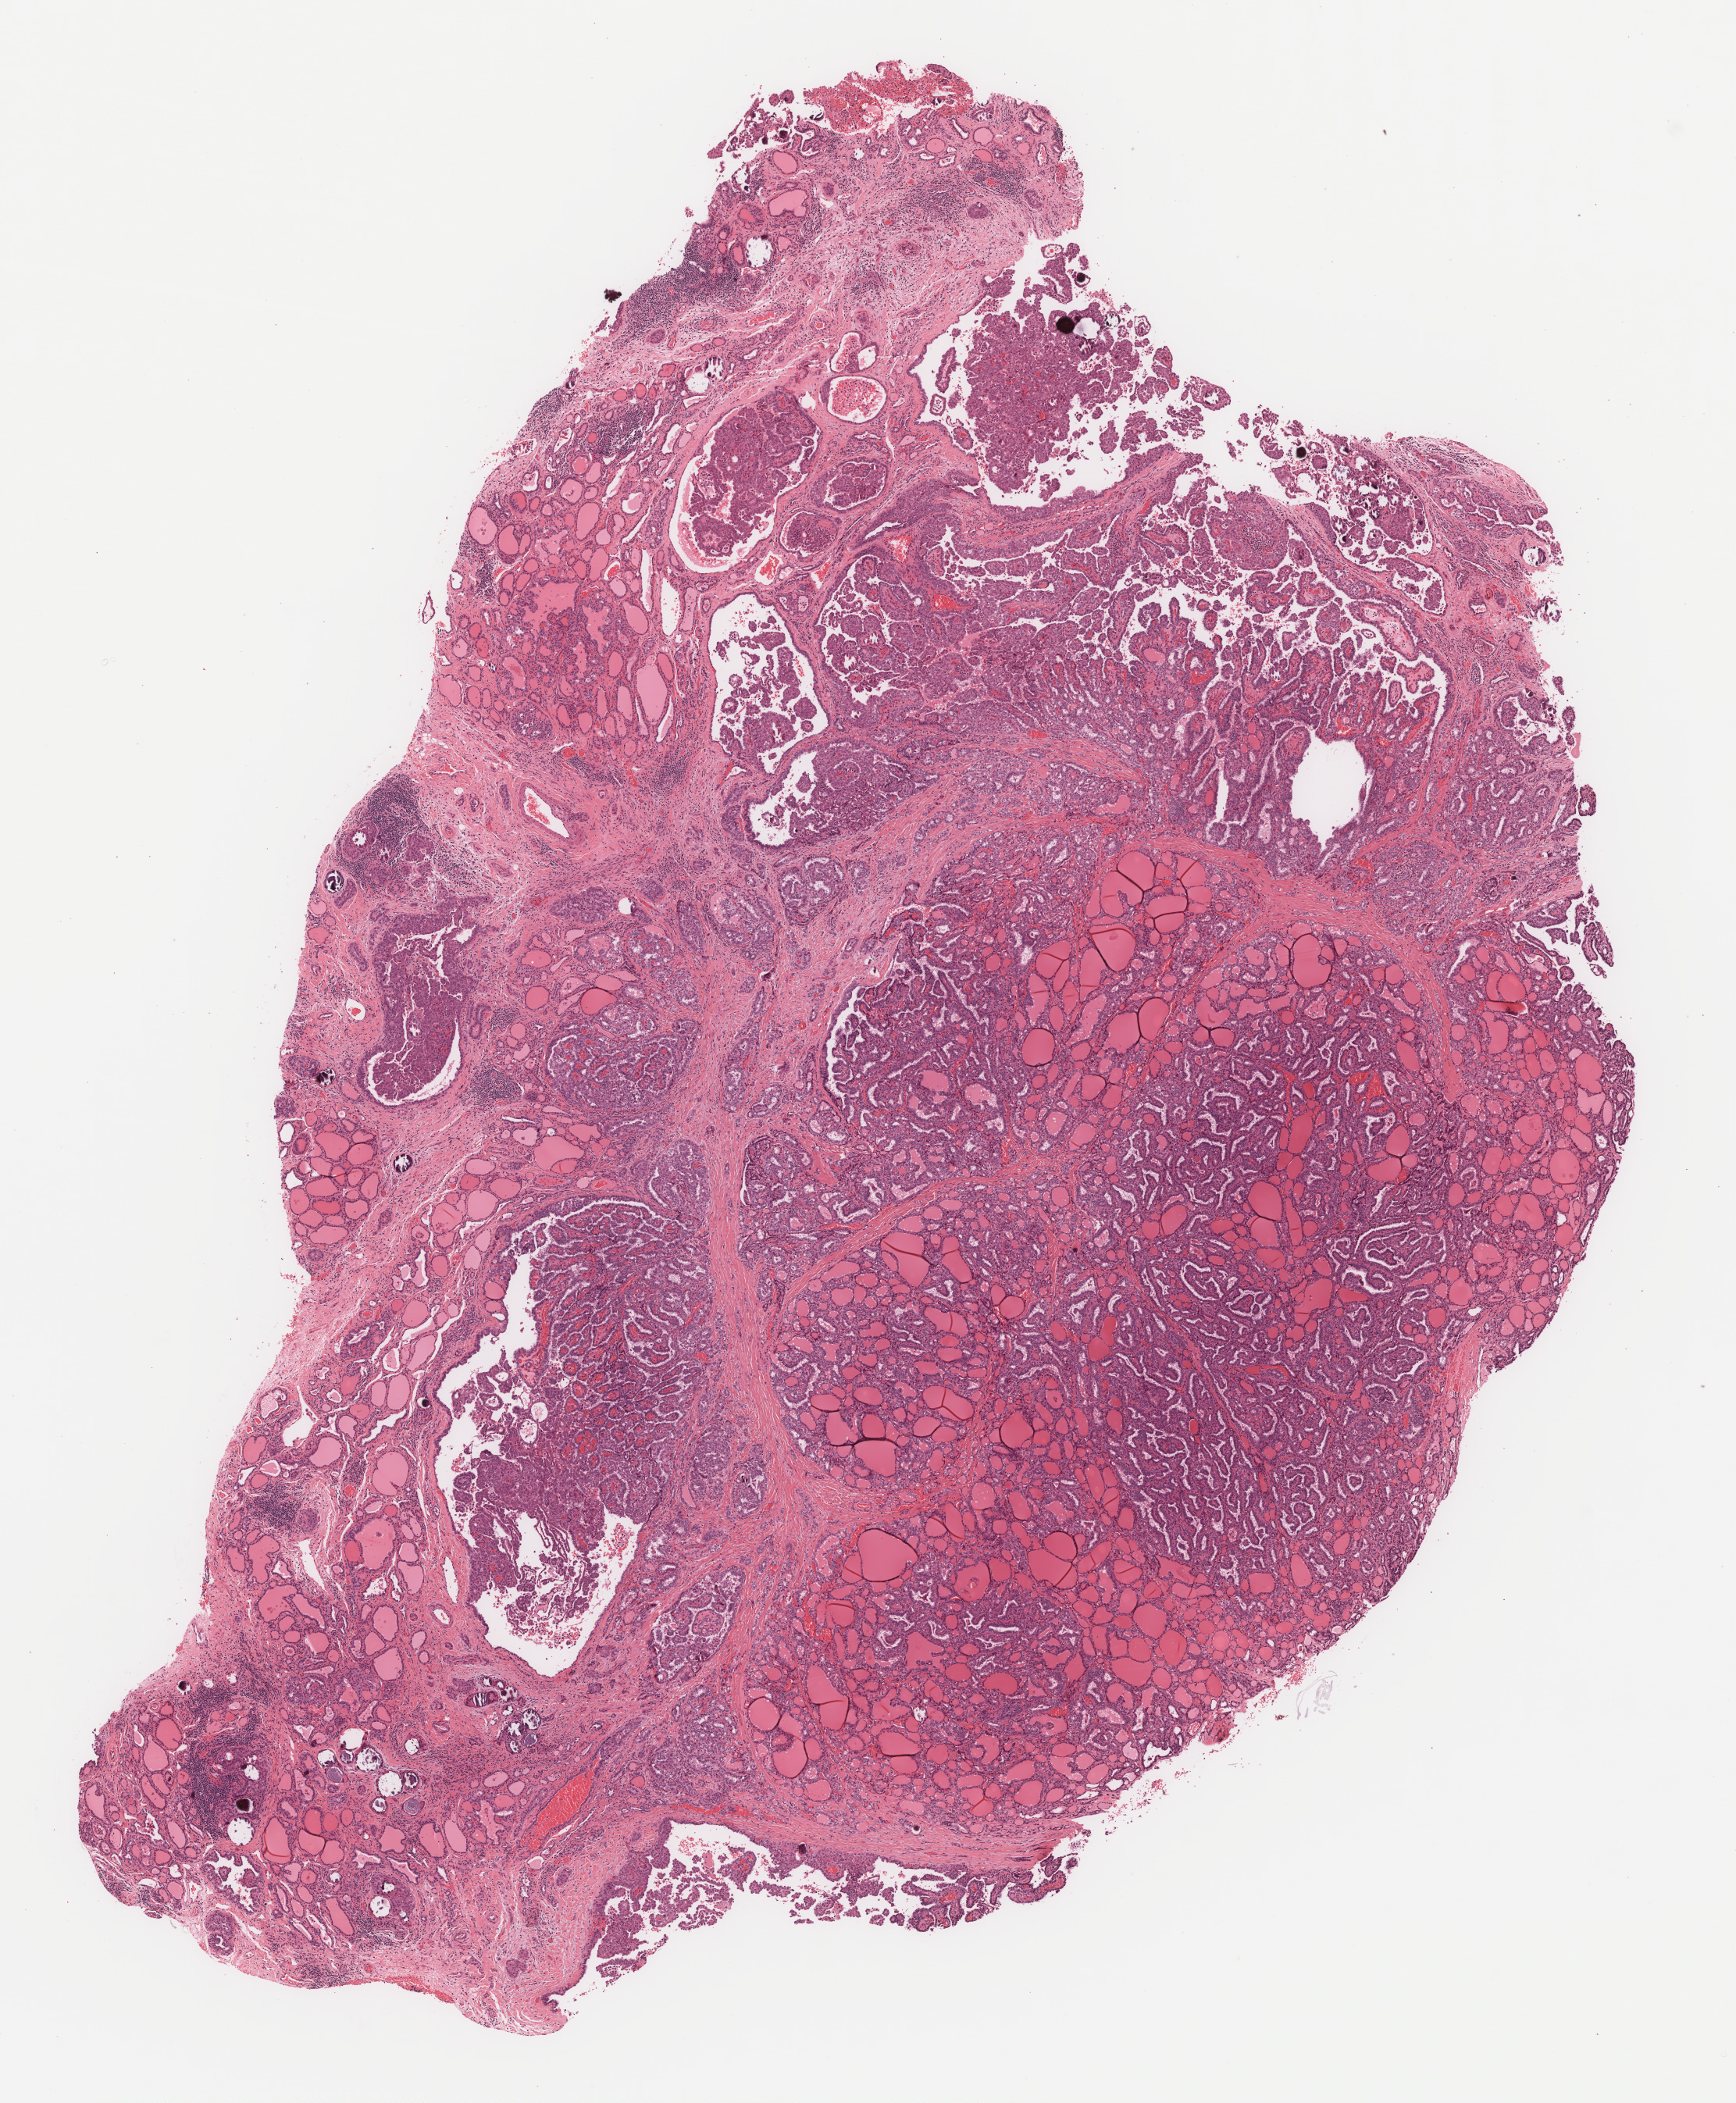
Whole-slide histology image, H&E — a low-resolution overview of the entire scanned area, about 9.0 x 10.8 mm; FFPE section; primary tumour sample from the thyroid. Patient: female, age at initial diagnosis 19 years.
Pathologic diagnosis: Papillary adenocarcinoma, NOS (thyroid gland).